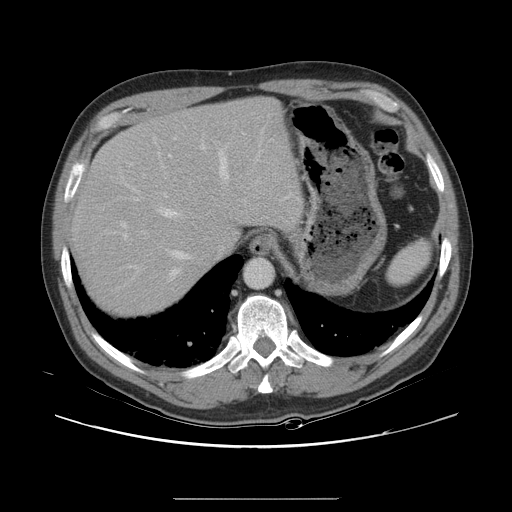
Contrast-enhanced abdominal CT, one axial slice; slice 24 of 40 in the series (ordered by position); intravenous contrast given; soft-tissue window (W 400 / L 40 HU); 5 mm slice thickness; 512 × 512 image matrix. Male patient, age 64 years. Case-level facts recorded for this patient, not image findings: diagnosis: colorectal cancer liver metastases, imaged before liver resection; multiple liver metastases: yes; largest metastasis: 3.2 cm; chemotherapy before resection: yes.
Annotated regions visible in this slice (manually delineated by an expert):
- hepatic veins: bounding box [x1, y1, x2, y2] px = [120, 137, 263, 279]
- liver: [72, 98, 297, 316]
- planned liver remnant (the part of the liver to remain after resection): [72, 98, 297, 270]
- portal vein (with intrahepatic branches): [121, 144, 209, 239]